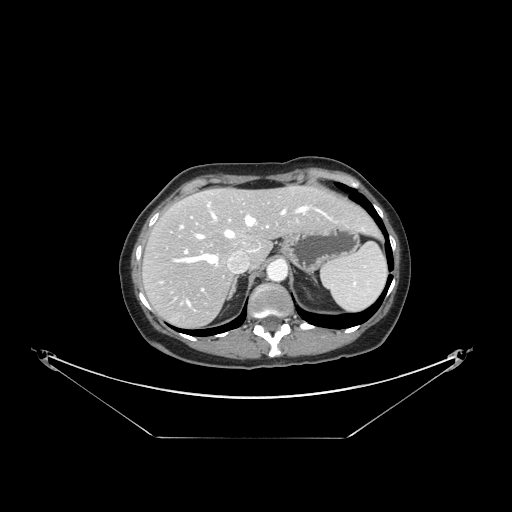
Contrast-enhanced abdominal CT, one axial slice; position 112 of 148 along the scan axis; reconstruction kernel STANDARD; 120 kVp; soft-tissue window (W 400 / L 40 HU); 2.5 mm slice thickness; 512 × 512 image matrix. Female patient, age 73 years. From the clinical record (not read from this slice): diagnosis: colorectal cancer liver metastases, imaged before liver resection; multiple liver metastases: no.
Outlined on this slice (manually delineated by an expert):
- hepatic veins: bounding box (x1, y1, x2, y2) in pixels: (175, 202, 309, 305)
- liver: (144, 187, 376, 327)
- planned liver remnant (the part of the liver to remain after resection): (168, 187, 376, 263)
- portal vein (with intrahepatic branches): (184, 209, 331, 291)